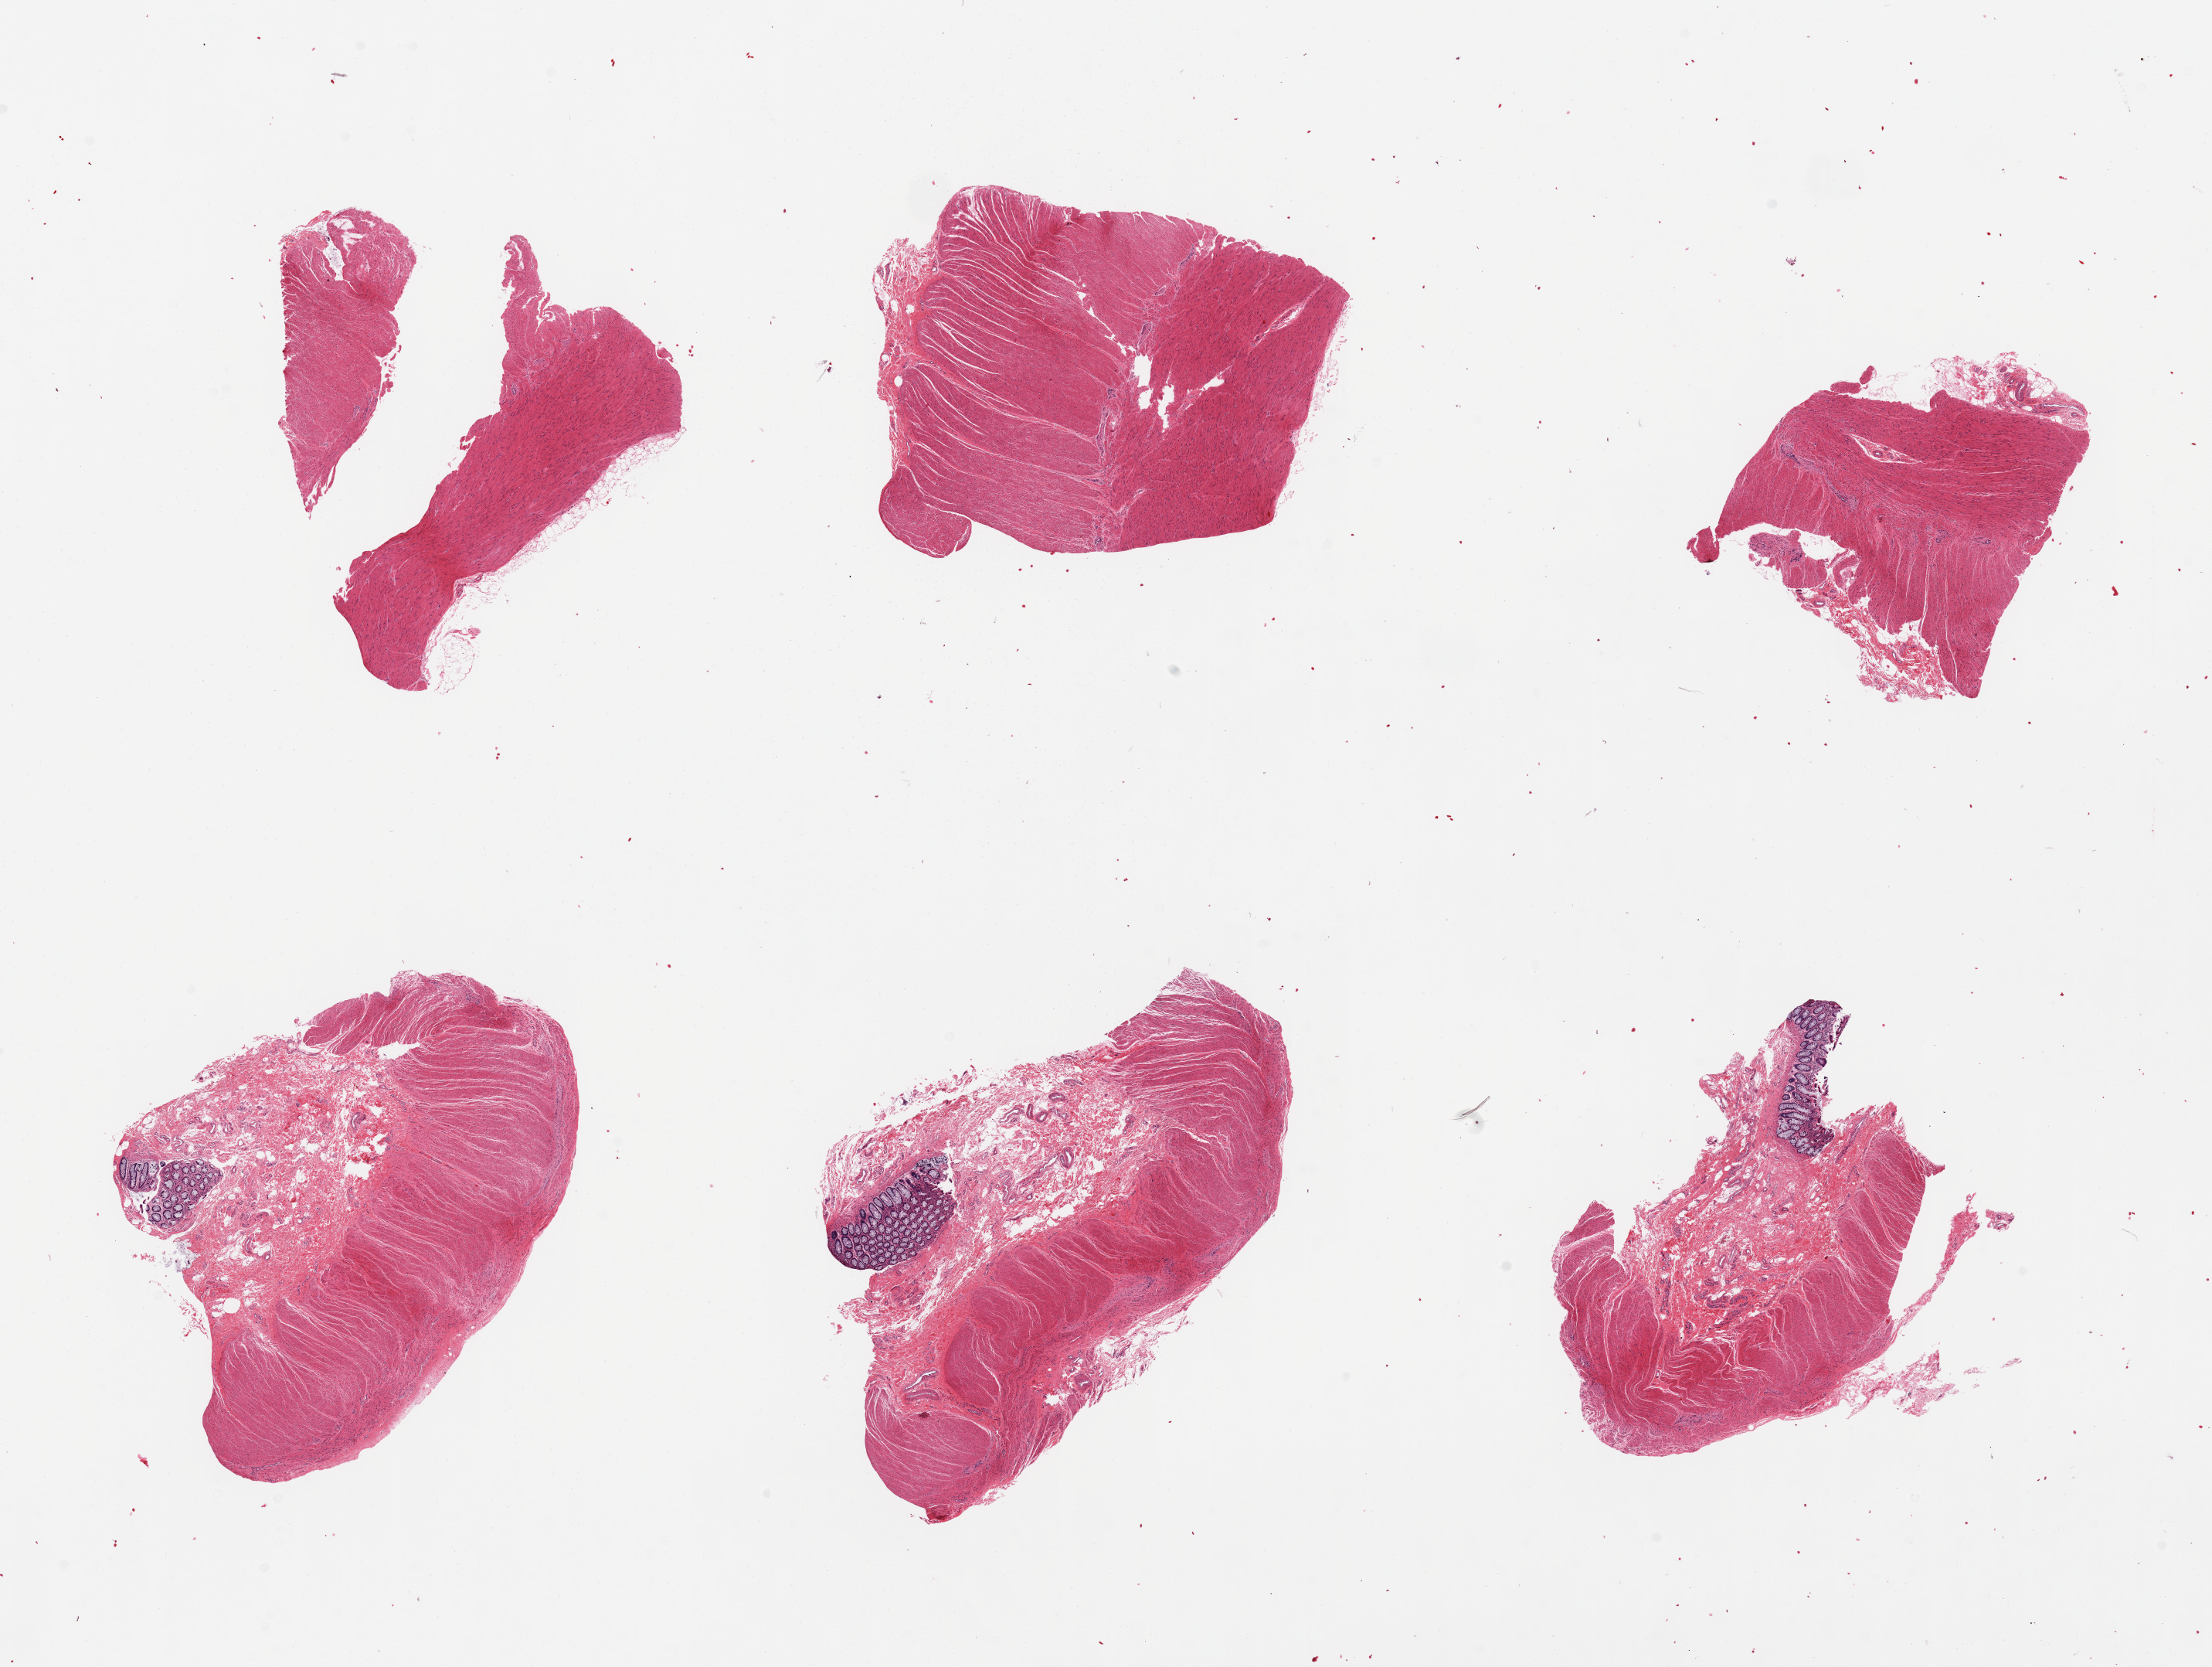
Digitized hematoxylin and eosin (H&E)-stained section — low-resolution overview of the scanned area, about 22.6 x 17.1 mm (acquisition: 20x scan). PAXgene-fixed, paraffin-embedded tissue. Target tissue: sigmoid colon. Tissue donor sample. Donor sex: female.
• reviewer comment on this tissue sample: 7 pieces, predominantly muscularis (target) with few strips of mucosa (not target)